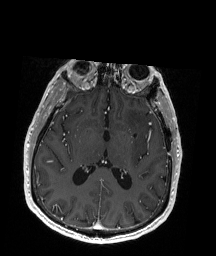
Brain MRI from a brain-tumour surgery series, one axial slice. Position 93 of 192 along the scan axis. T1-weighted post-contrast. 1 mm slice thickness. 216 × 256 image matrix. From the clinical record (not read from this slice): histopathology: Oligodendroglioma; WHO grade: 2; IDH mutation: yes.
Outlined on this slice (manually delineated by an expert):
- previous resection cavity: box from (x=145, y=131) to (x=149, y=135) px